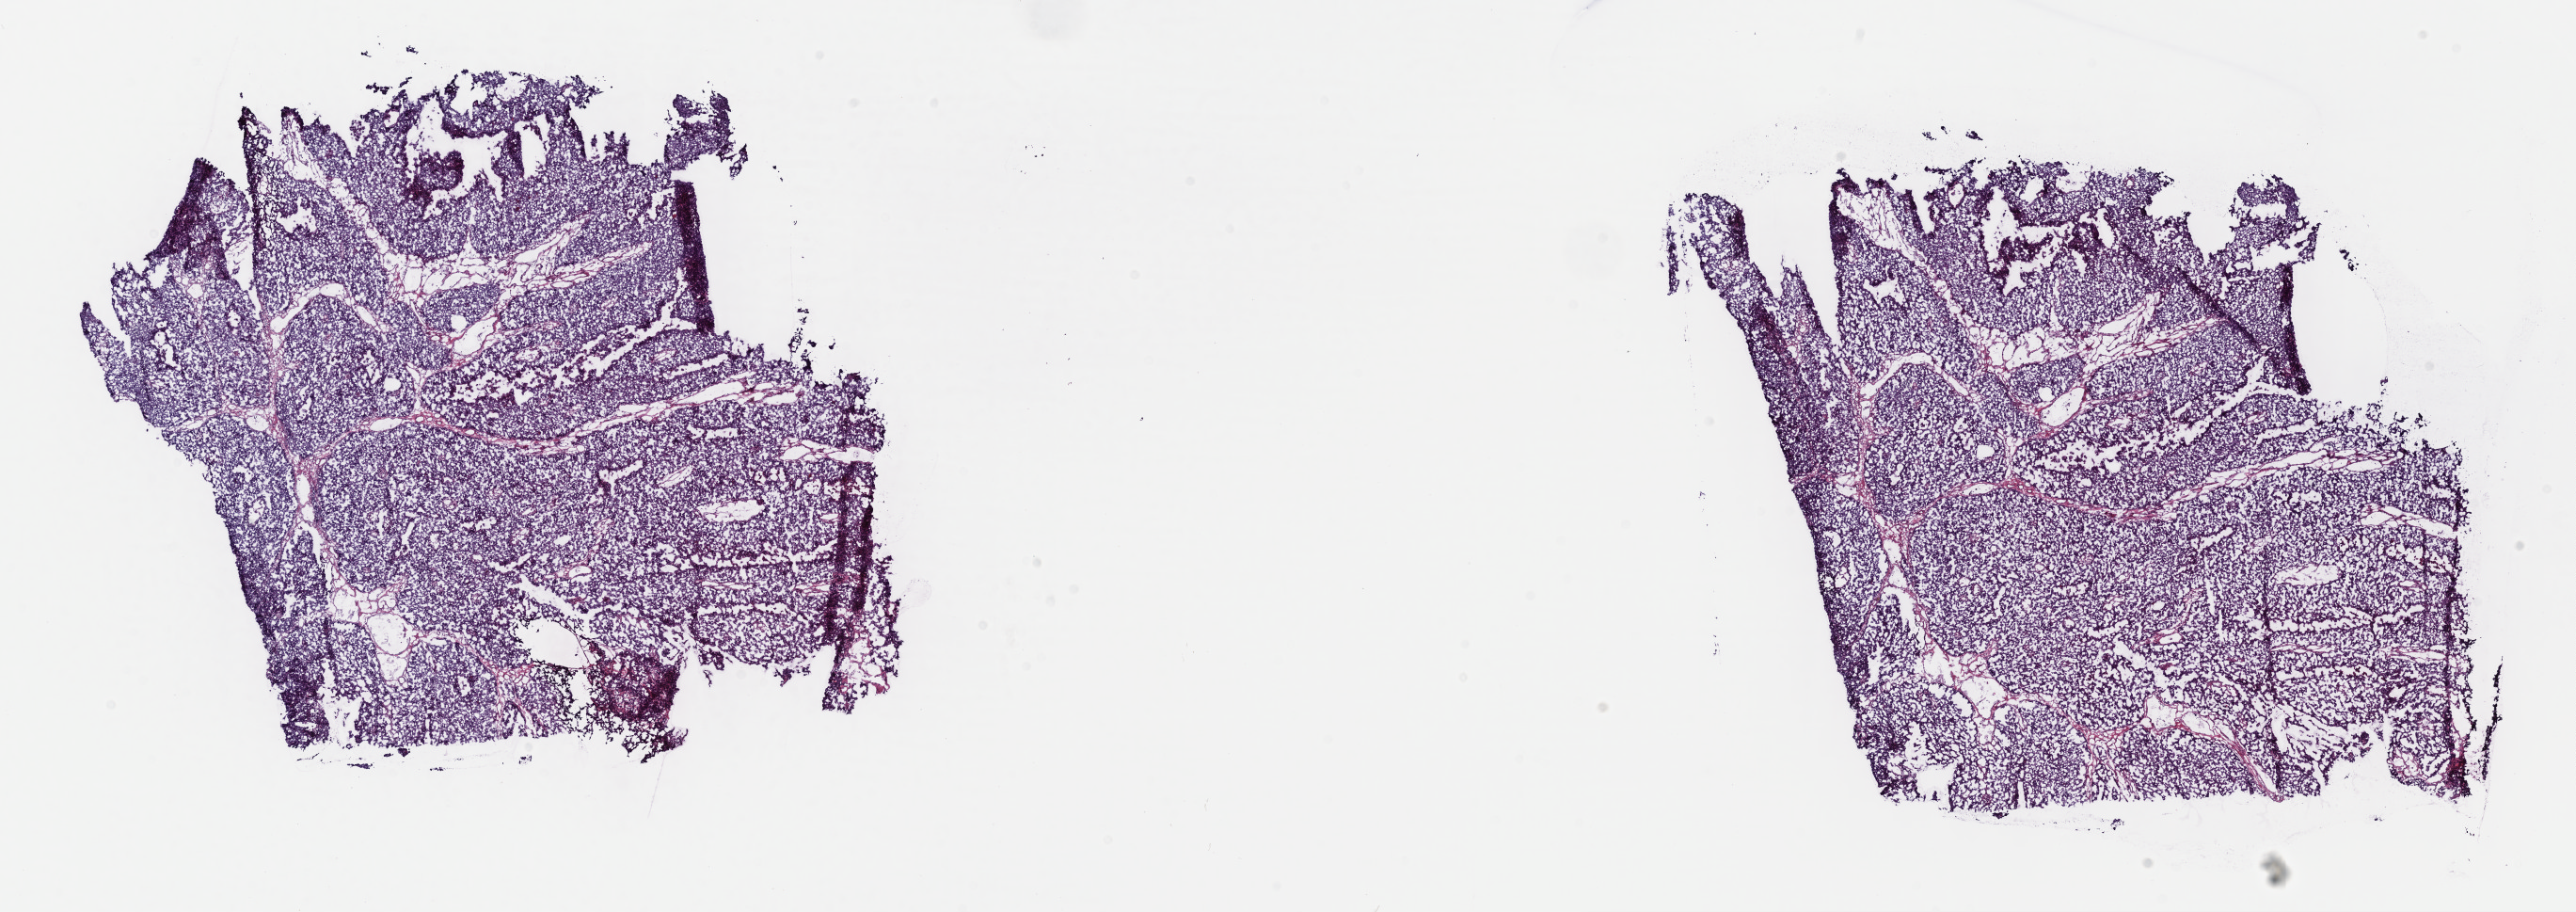
Whole-slide histology image, Hematoxylin and eosin (H&E) stained, a low-resolution overview of the entire scanned area, about 22.1 x 7.8 mm (slide scanned at 40x). Frozen section from the top of the tissue portion. Primary tumour sample from the bladder. Male patient; age at initial diagnosis 82 years. Histologic grade: high grade. Pathologist review of this section (percent, as recorded): tumour cells 100%, tumour nuclei 80%, normal cells 0%, stromal cells 0%, necrosis 0%. Infiltration values recorded for this section: lymphocyte infiltration 2%, monocyte infiltration 0%, neutrophil infiltration 0%.
- TNM: T3 N0 M0
- histologic diagnosis: Transitional cell carcinoma (anterior wall of bladder)
- AJCC pathologic stage: III (7th edition)